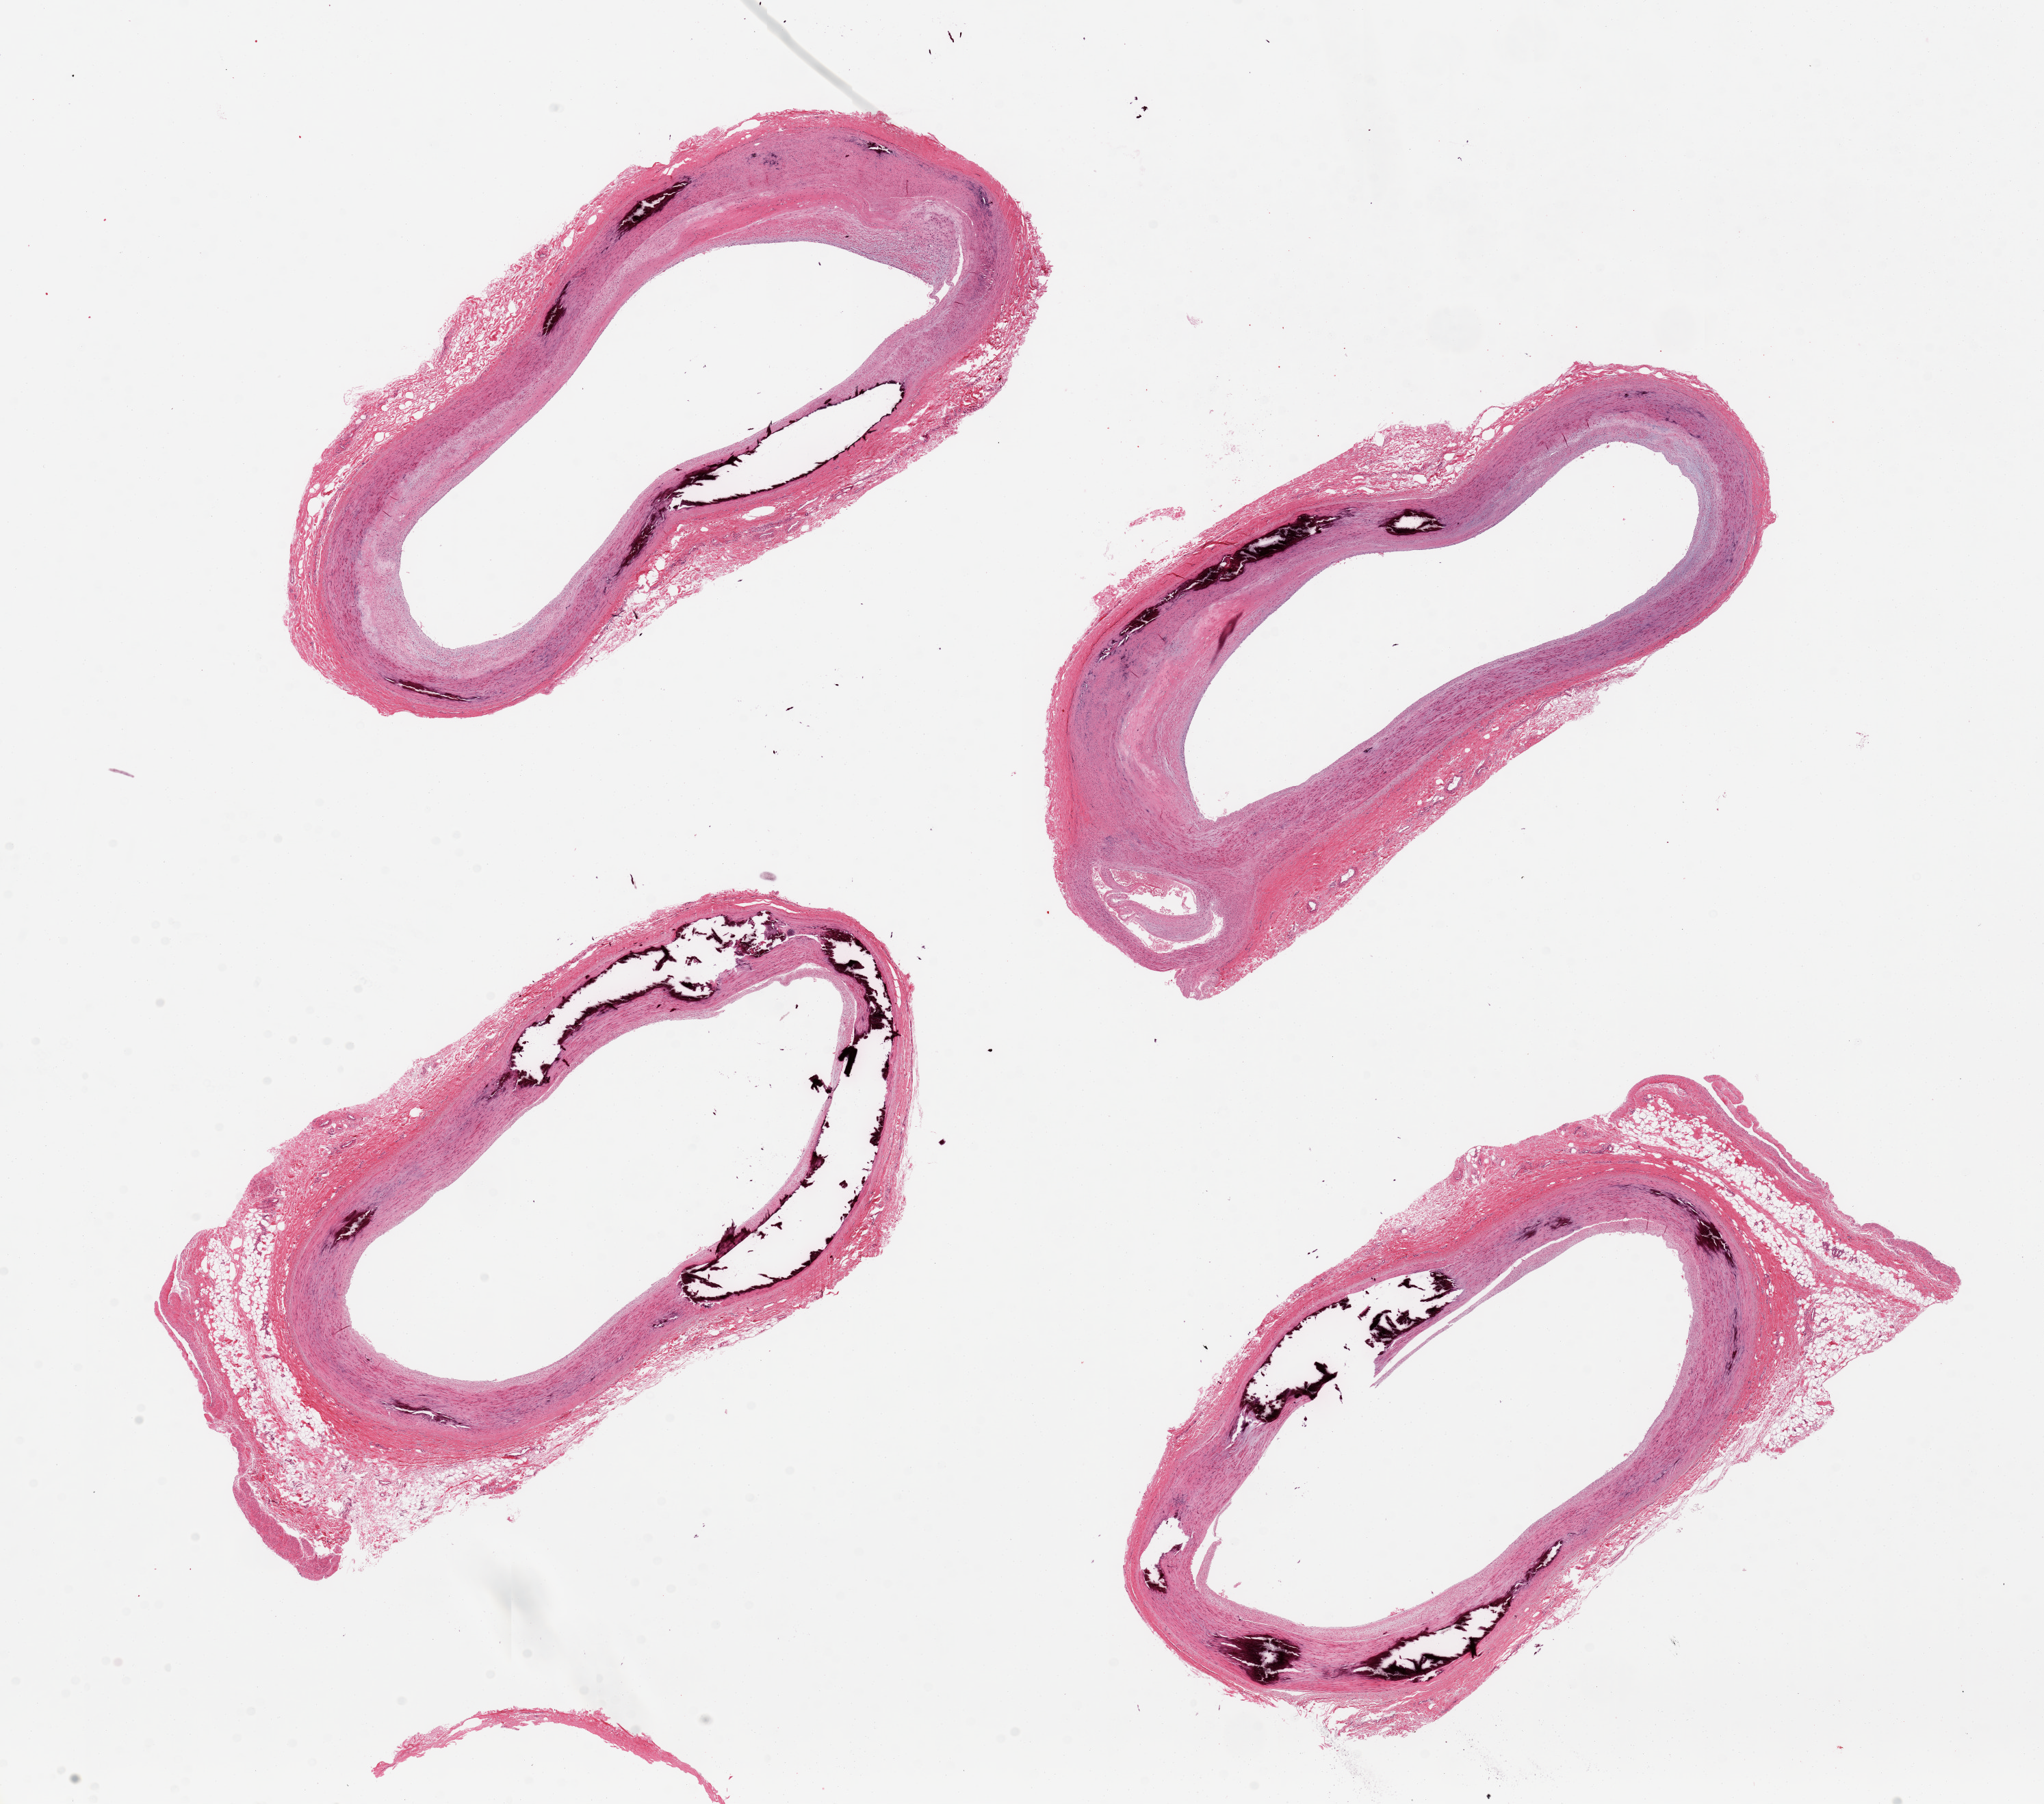
Digitized H&E-stained section — a low-resolution overview of the entire scanned area, about 23.6 x 20.9 mm. PAXgene-fixed, paraffin-embedded tissue. Target tissue: tibial artery. Donor tissue sample. Male donor.
• pathologist's review note for this sample: 4 pieces; all heavily calcified medially; no luminal plaques; up to 1 mm external fat